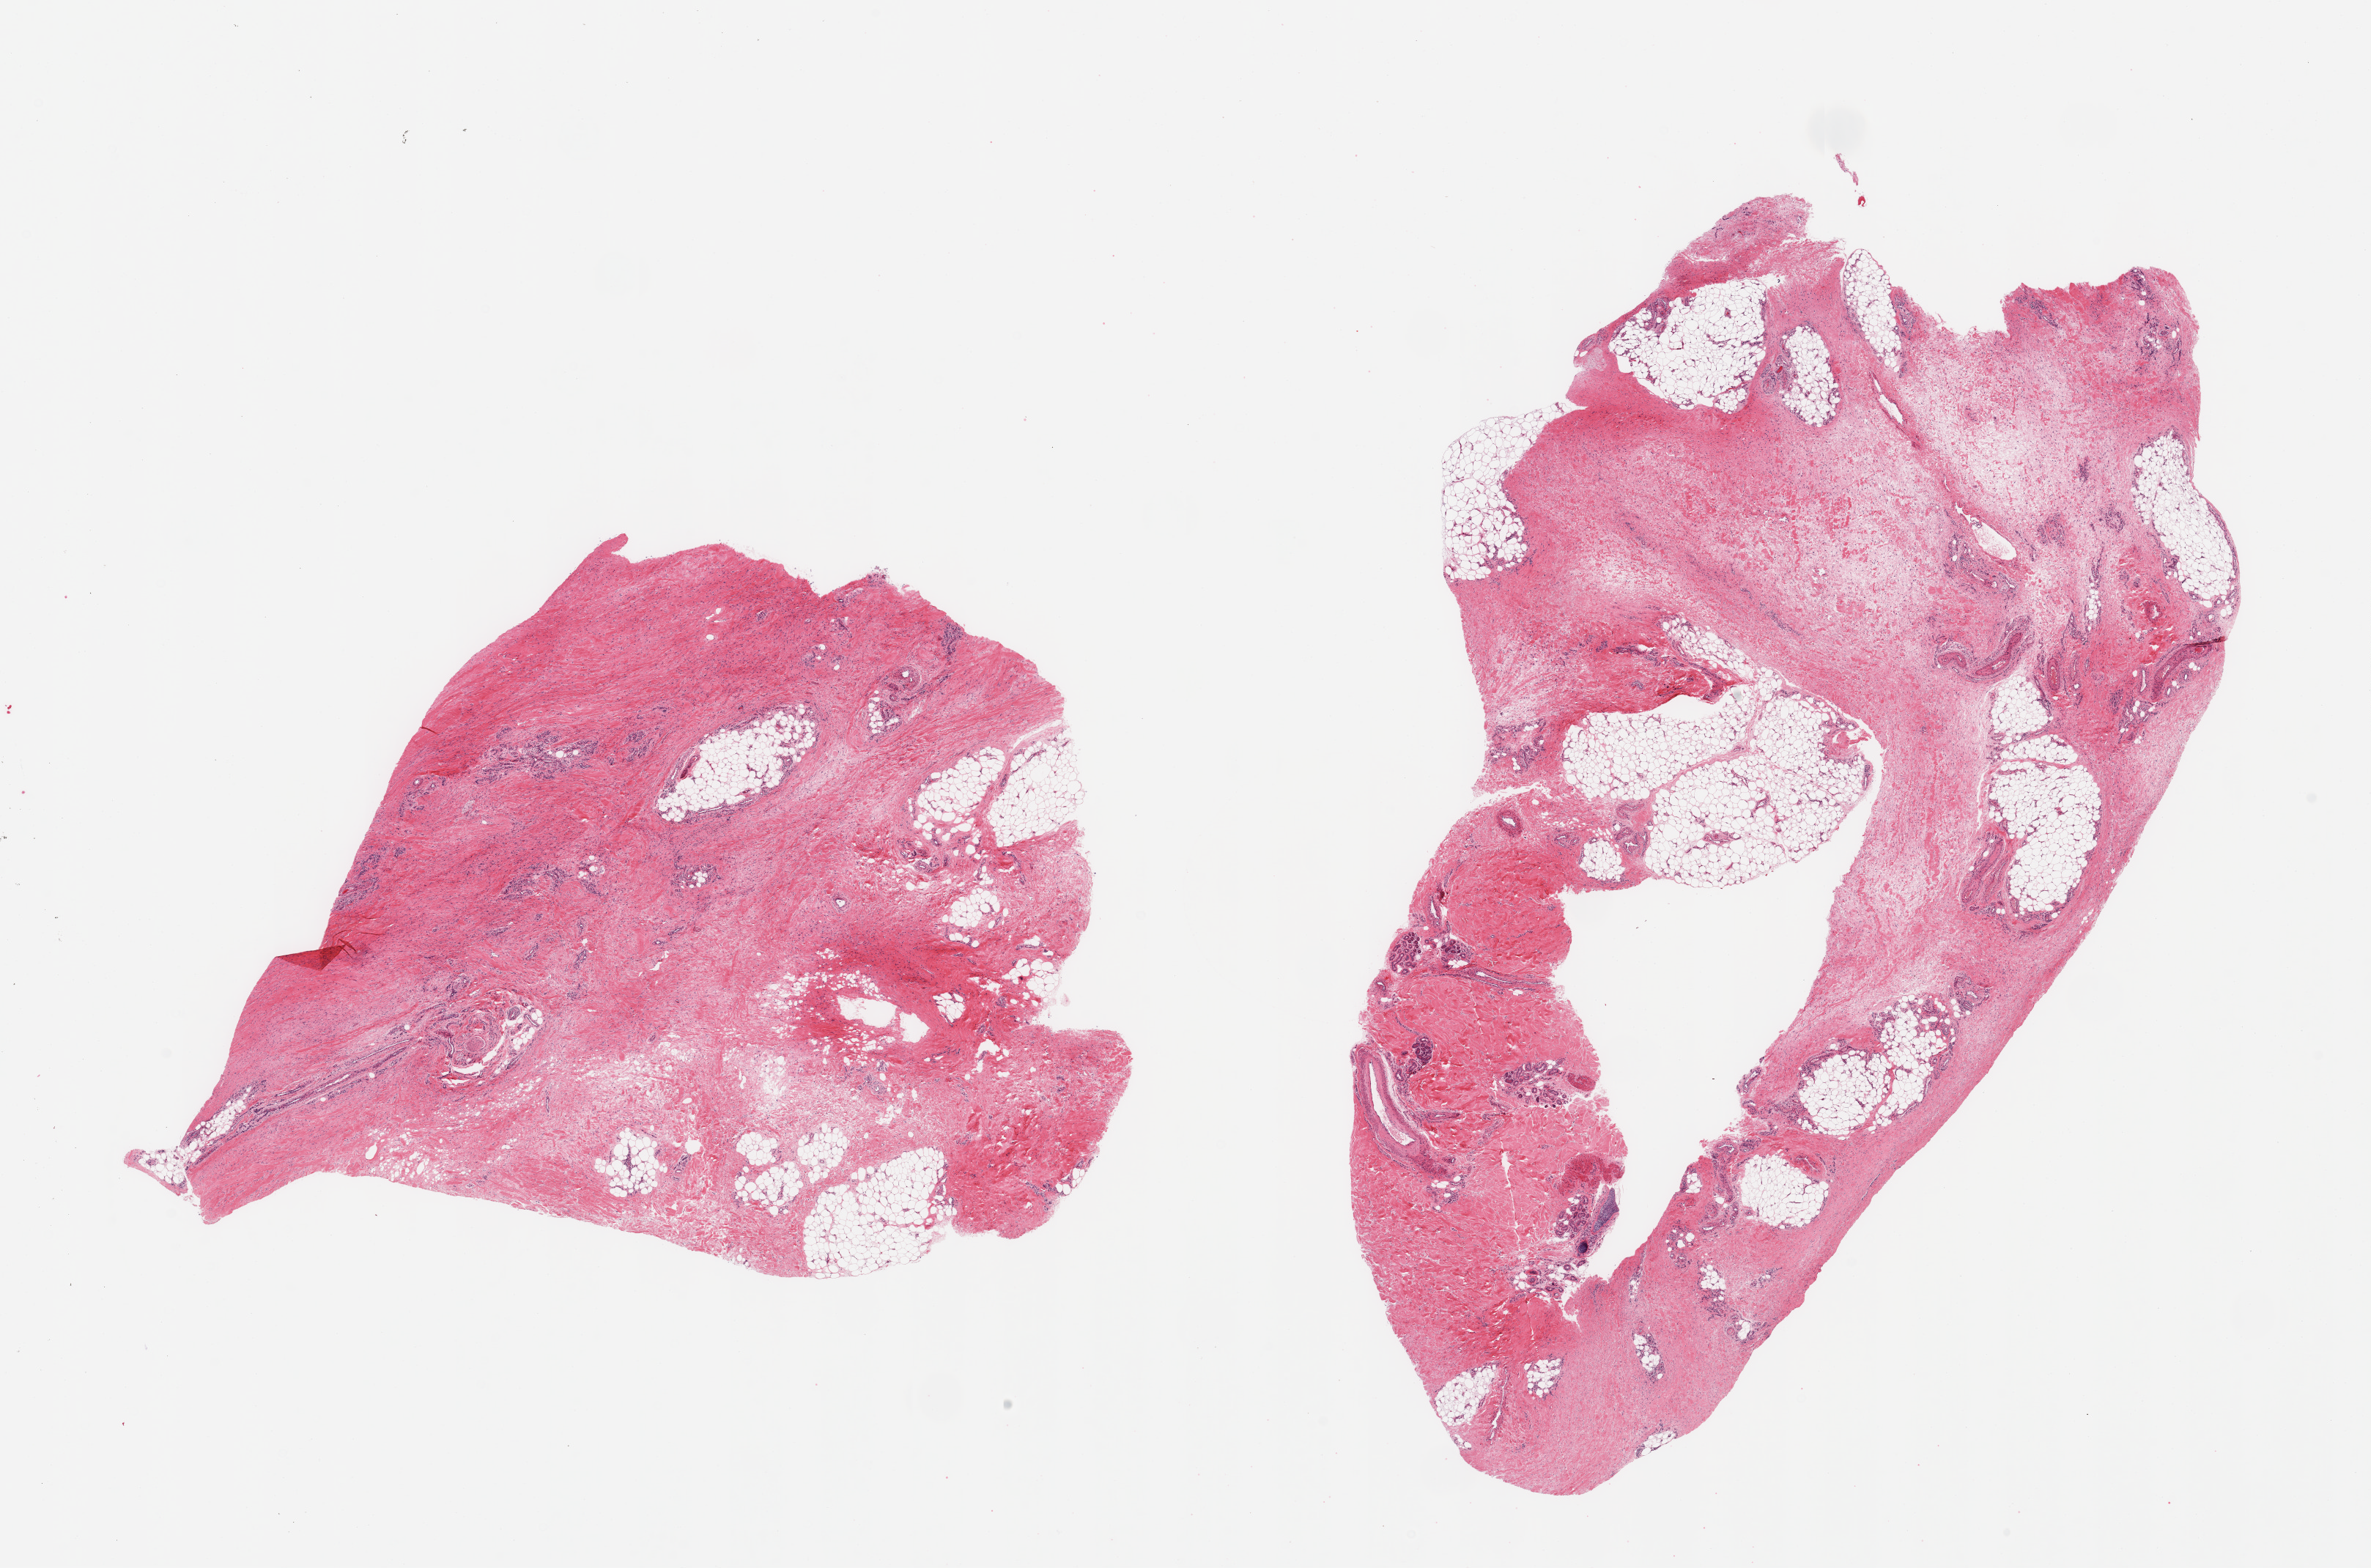
Whole-slide image, hematoxylin and eosin (H&E) stain, whole scanned area (about 25.6 x 16.9 mm, slide scanned at 20x) shown as a low-resolution overview. Donor: male.
Specimen: PAXgene-fixed, paraffin-embedded tissue; sampled site (target tissue): adipose tissue; tissue donor sample.